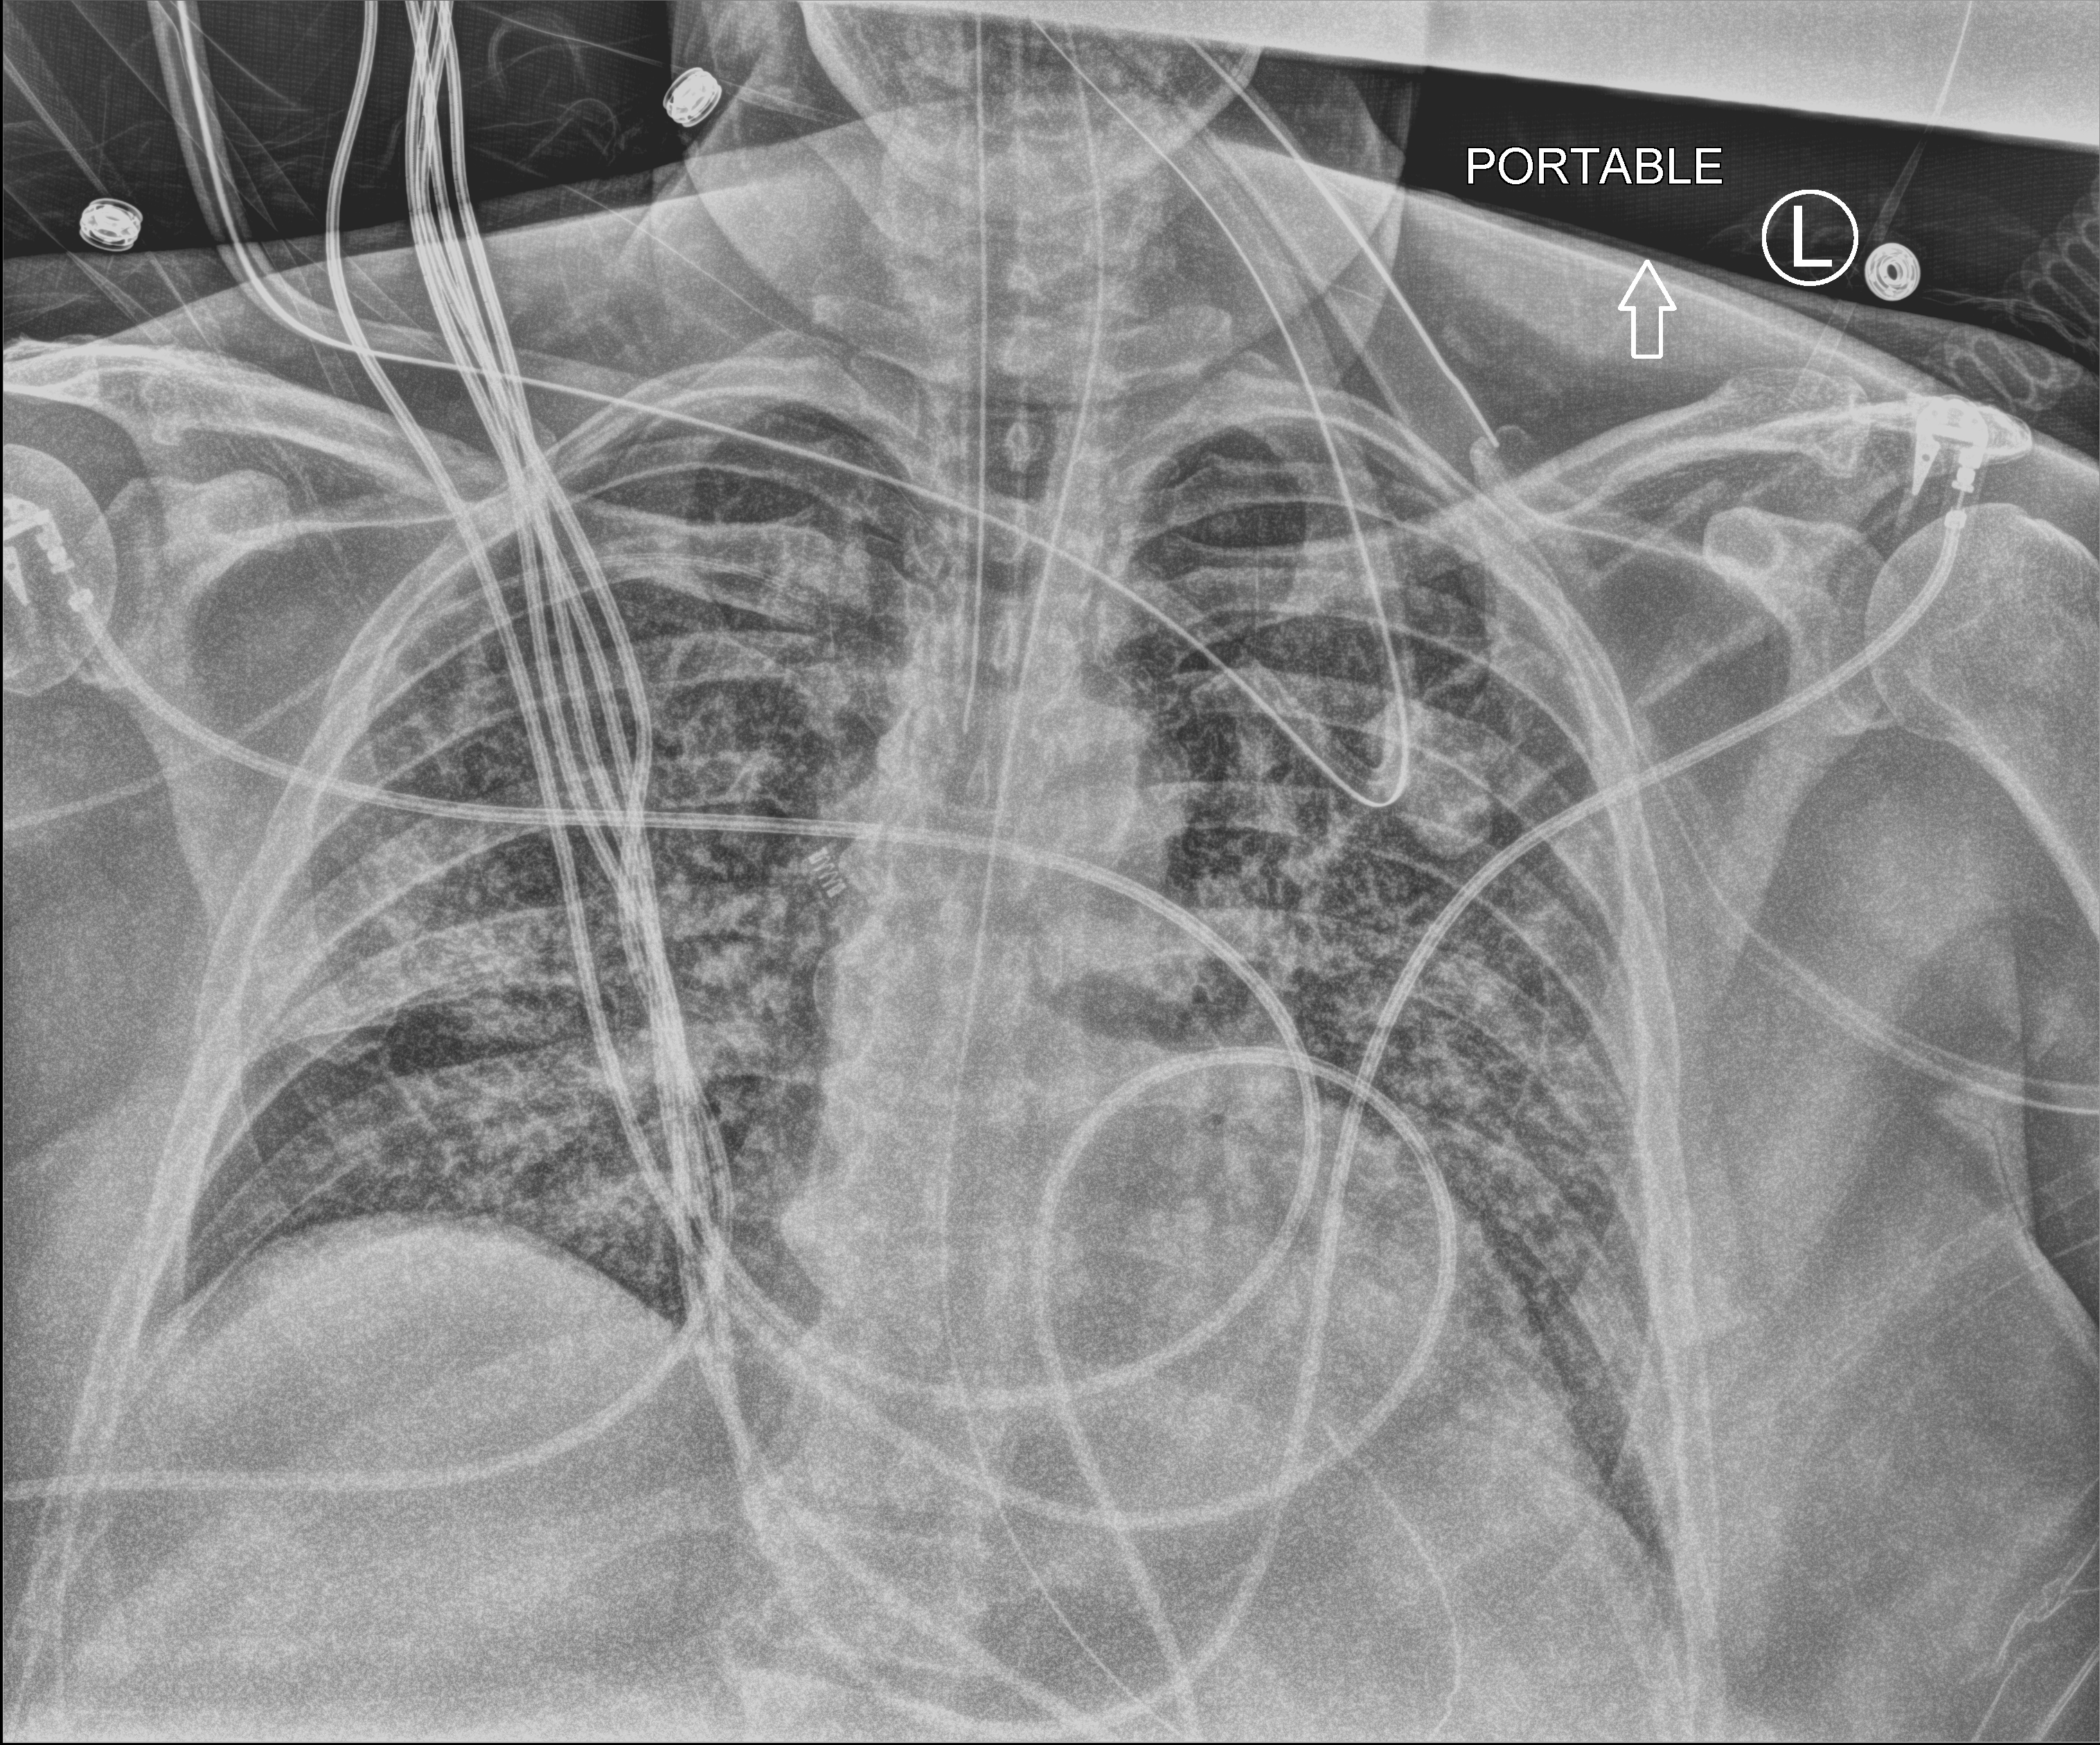
Portable chest radiograph. Patient hospitalised with COVID-19, aged 18–59 years.
Hospital-stay facts (about this admission, not read from this image; timing relative to this image not recorded): mechanically ventilated during this hospital stay: yes.